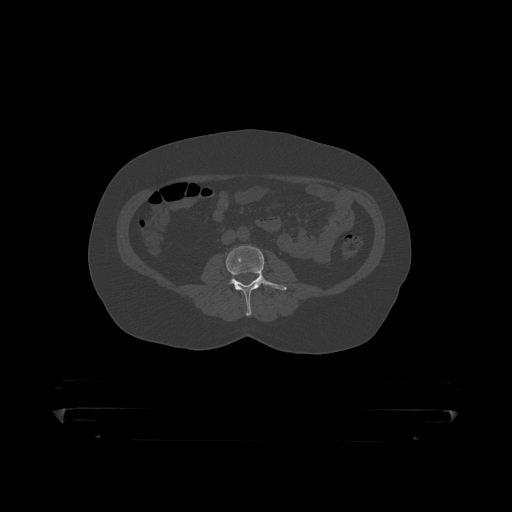
CT including the spine, one axial slice. Slice 88 of 390 in the series (ordered by position). Bone window (W 1800 / L 400 HU). 512 × 512 image matrix, field of view 650 × 650 mm. Male patient, age 60 years. From the clinical record (not read from this slice): primary cancer: prostate.
Structures marked on this image (semi-automatic segmentation, software-assisted and operator-edited):
- L3 vertebra: box from (x=226, y=246) to (x=288, y=316) px